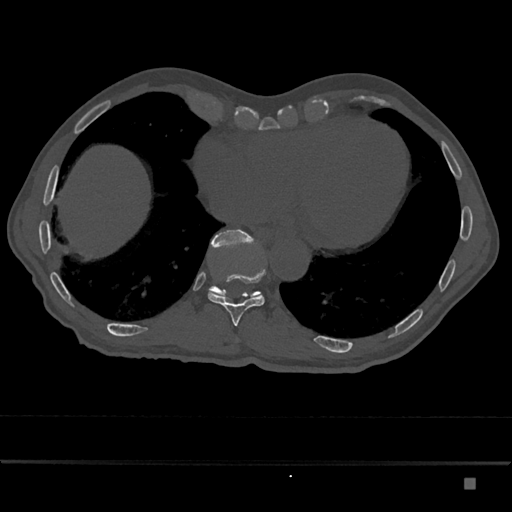
CT including the spine, one axial slice. Slice 727 of 797 in the series (ordered by position). Reconstruction kernel Br40s/3. 120 kVp. Bone window (W 1800 / L 400 HU). 512 × 512 image matrix, field of view 390 × 390 mm. Male patient, age 72 years. Case-level facts recorded for this patient, not image findings: primary cancer: prostate.
Outlined on this slice (semi-automatically segmented with operator editing):
- T10 vertebra: box from (x=208, y=269) to (x=266, y=326) px
- T11 vertebra: (x=208, y=229)–(x=261, y=300)